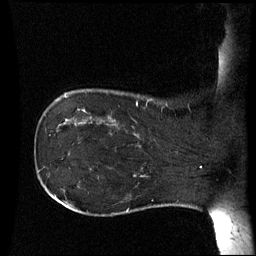
Breast MRI (dynamic contrast-enhanced), one sagittal slice. Position 12 of 60 along the scan axis. Dynamic contrast-enhanced series, image 2 of 3 at this slice position (ordered by acquisition). 1.5 T. TE 4.2 ms, TR 8.9 ms. 2.5 mm slice thickness. 256 × 256 image matrix. Female patient, age 42 years. Case-level facts recorded for this patient, not image findings: setting: breast cancer imaged before/during neoadjuvant chemotherapy; receptor status: HER2-positive.
Outlined on this slice (semi-automatically segmented with operator editing):
- analysis volume of interest (the breast-tissue region the enhancement analysis was run in; not a lesion): bounding box (x1, y1, x2, y2) in pixels: (106, 102, 173, 150)
- tumour enhancement mask (voxels above the 70 % enhancement threshold inside the analysis volume of interest): (136, 102, 138, 107)